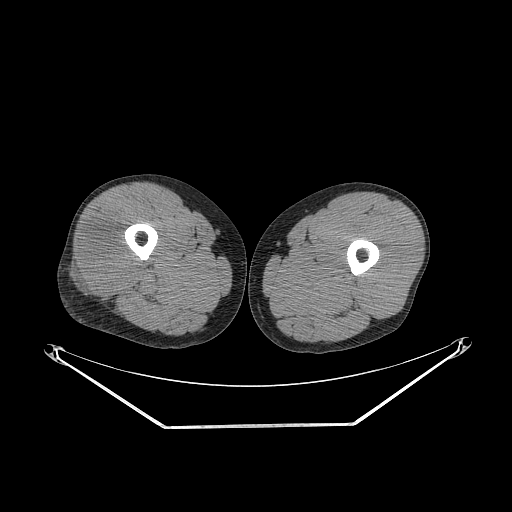
CT of an extremity soft-tissue mass (from a PET/CT study), one axial slice. Slice 239 of 267 in the series (ordered by position). 140 kVp. Soft-tissue window (W 400 / L 40 HU). 3.75 mm slice thickness. 512 × 512 image matrix. Male patient. From the clinical record (not read from this slice): histological type: poorly differentiated synovial sarcoma; grade: high; site of the primary tumour: right buttock.
Structures marked on this image (expert contour drawn on MRI and transferred to this co-registered scan by the dataset authors):
- gross tumour volume including surrounding oedema: box from (x=73, y=222) to (x=134, y=293) px
- gross tumour volume (mass): (x=82, y=226)–(x=134, y=293)